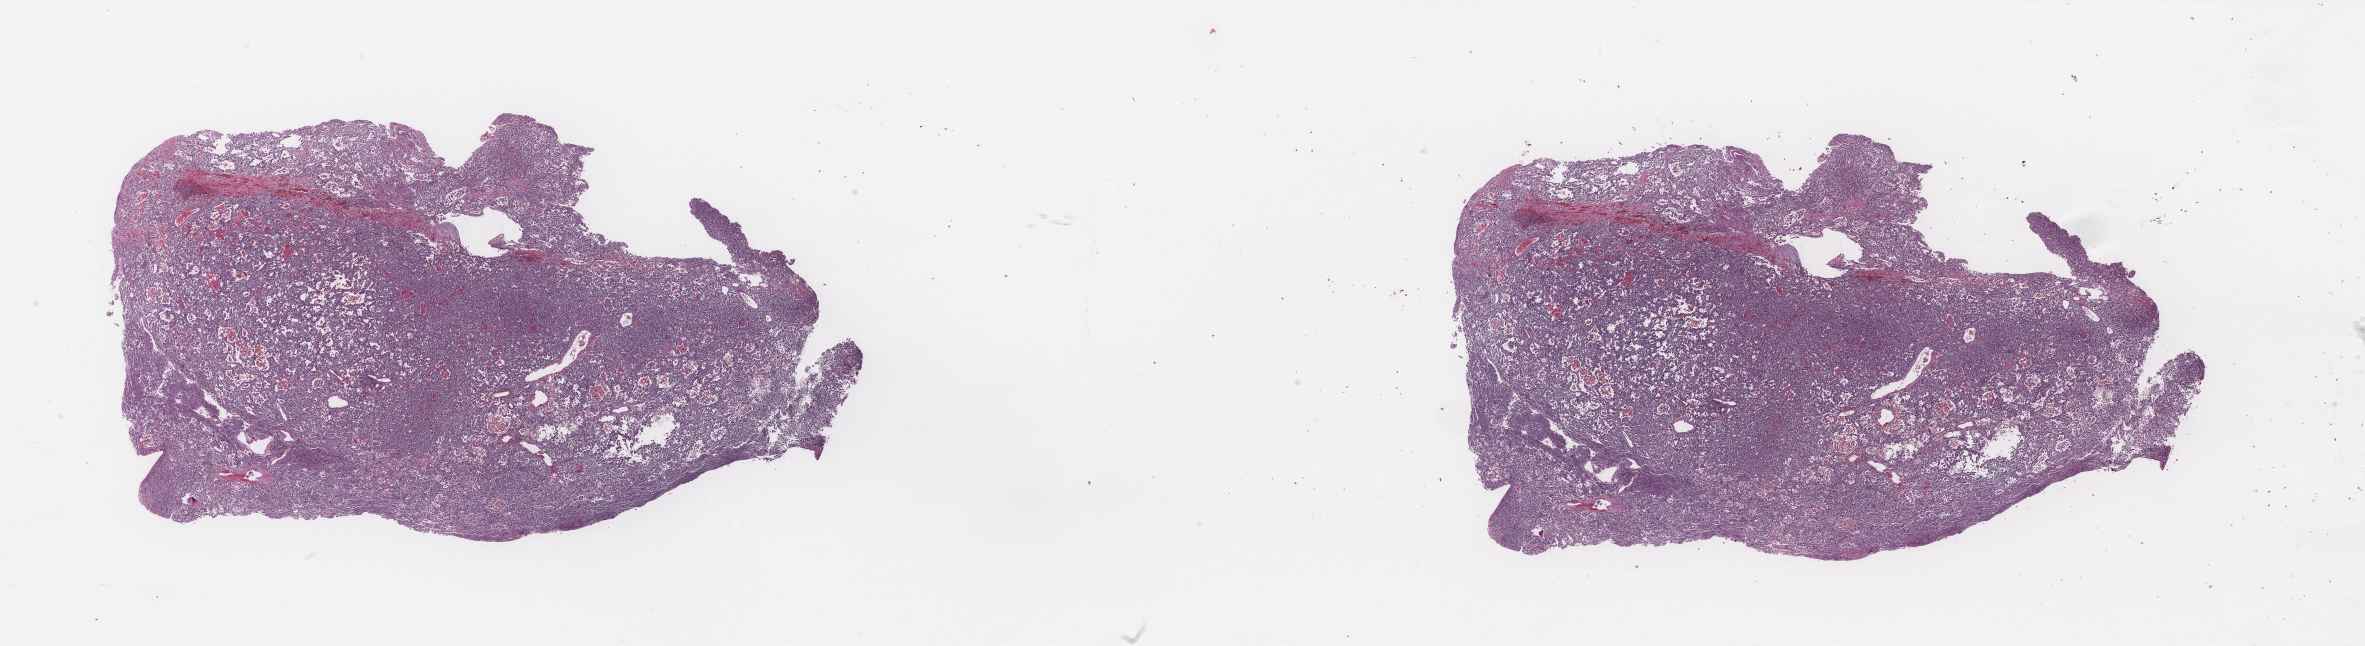
Whole-slide histology image, Hematoxylin and eosin (H&E) stained, whole scanned area (about 37.4 x 10.2 mm, from a 40x scan) shown as a low-resolution overview. Formalin-fixed paraffin-embedded (FFPE) diagnostic section. Sample: primary tumour, adrenal gland. Male patient; age at initial diagnosis 40 years.
Diagnosis: Pheochromocytoma, malignant (medulla of adrenal gland).